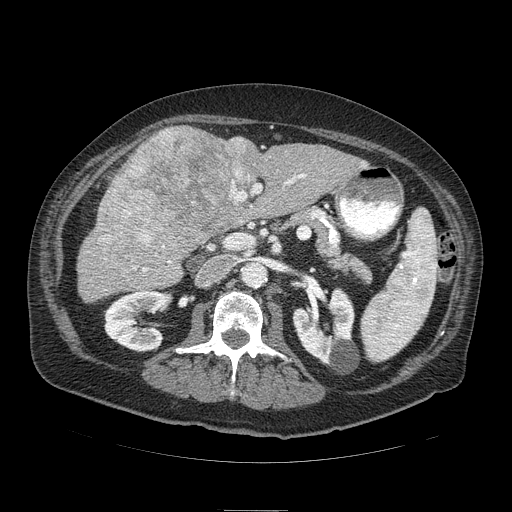
Contrast-enhanced abdominal CT (liver protocol), one axial slice. Slice 40 of 103 in the series (ordered by position). Reconstruction kernel STANDARD. 120 kVp. Soft-tissue window (W 400 / L 40 HU). 2.5 mm slice thickness. 512 × 512 image matrix. From the clinical record (not read from this slice): diagnosis: hepatocellular carcinoma (patient treated with transarterial chemoembolisation; whether this scan precedes or follows treatment is not stated here); TNM stage (as recorded): Stage-IIIA; Child-Pugh class: B; tumour differentiation: well differentiated; tumour nodularity: multinodular.
Annotated regions visible in this slice (semi-automatic segmentation, software-assisted and operator-edited):
- liver parenchyma outside the tumour (the mass and vessels are separate outlines, so this box may not span the whole liver): bounding box [x1, y1, x2, y2] px = [78, 126, 368, 302]
- mass: [93, 126, 259, 261]
- liver vessels: [133, 174, 306, 272]